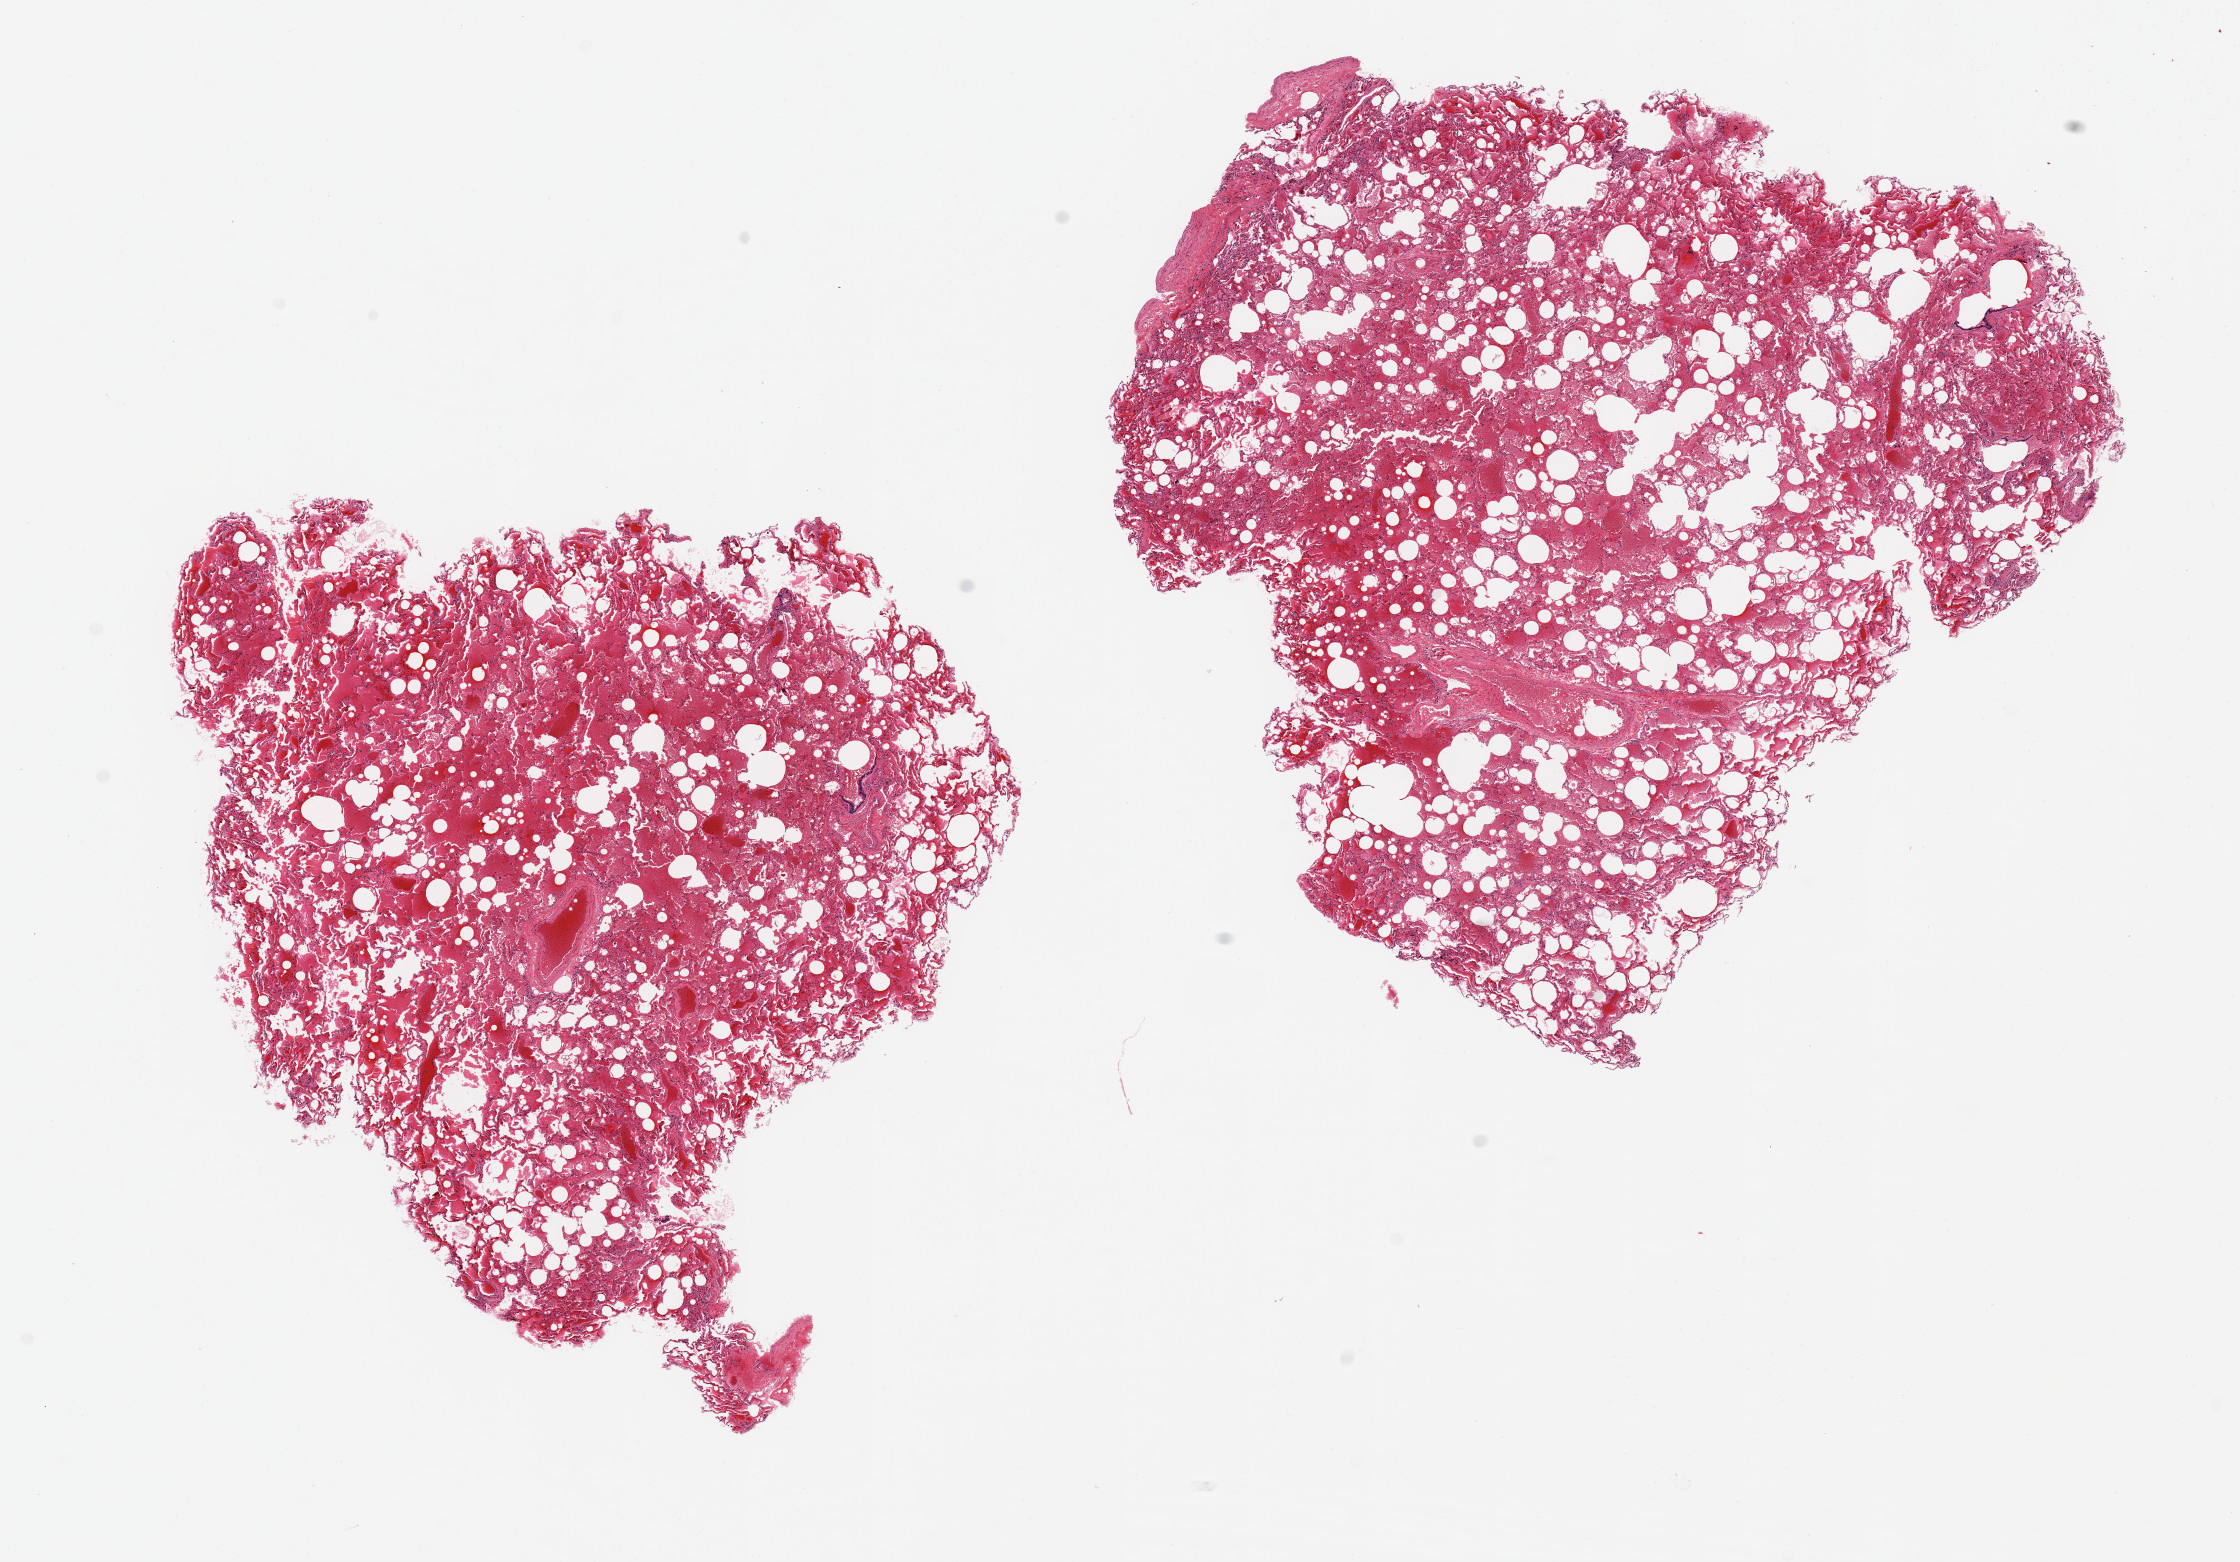
Digitized haematoxylin and eosin-stained section, brightfield — a low-resolution overview of the entire scanned area, about 17.7 x 12.4 mm, PAXgene-fixed, paraffin-embedded tissue, target tissue: lung, donor tissue sample. Donor: male.
Review note (as recorded): 2 ~7x6.5mm aliquots. Diffuse severe congestion/?hemorrhagic pneumonitis.